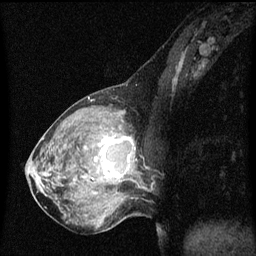
Breast MRI (dynamic contrast-enhanced), one sagittal slice. Position 26 of 60 along the scan axis. Dynamic contrast-enhanced series, image 2 of 3 at this slice position (ordered by acquisition). 1.5 T. TE 4.2 ms, TR 8 ms. 2 mm slice thickness. 256 × 256 image matrix, field of view 200 × 200 mm. Patient: female, 50 years.
Structures marked on this image (semi-automatic segmentation, software-assisted and operator-edited):
- analysis volume of interest (the breast-tissue region the enhancement analysis was run in; not a lesion): bounding box (x1, y1, x2, y2) in pixels: (91, 126, 141, 189)
- tumour enhancement mask (voxels above the 70 % enhancement threshold inside the analysis volume of interest): (92, 136, 134, 181)